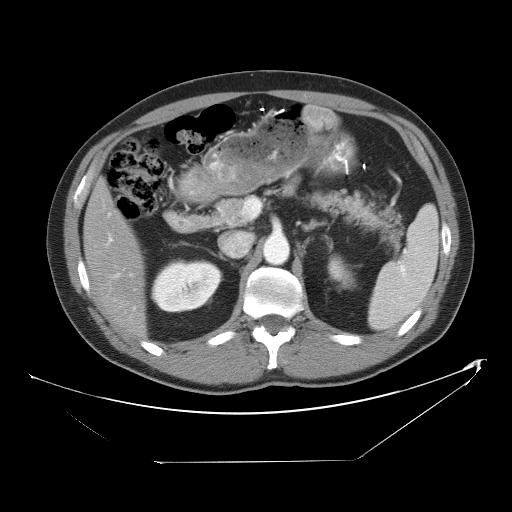
Contrast-enhanced abdominal CT, one axial slice. Slice 27 of 53 in the series (ordered by position). Reconstruction kernel STANDARD. 120 kVp. Intravenous contrast given. Soft-tissue window (W 400 / L 40 HU). 512 × 512 image matrix. Male patient, age 59 years. Case-level facts recorded for this patient, not image findings: diagnosis: colorectal cancer liver metastases, imaged before liver resection; multiple liver metastases: yes; largest metastasis: 8.5 cm; disease in both lobes: no.
Annotated regions visible in this slice (expert manual segmentation):
- hepatic veins: bounding box <108,213,120,277> (left, top, right, bottom; pixels)
- liver: <84,185,144,335>
- planned liver remnant (the part of the liver to remain after resection): <84,185,144,335>
- portal vein (with intrahepatic branches): <108,237,113,243>